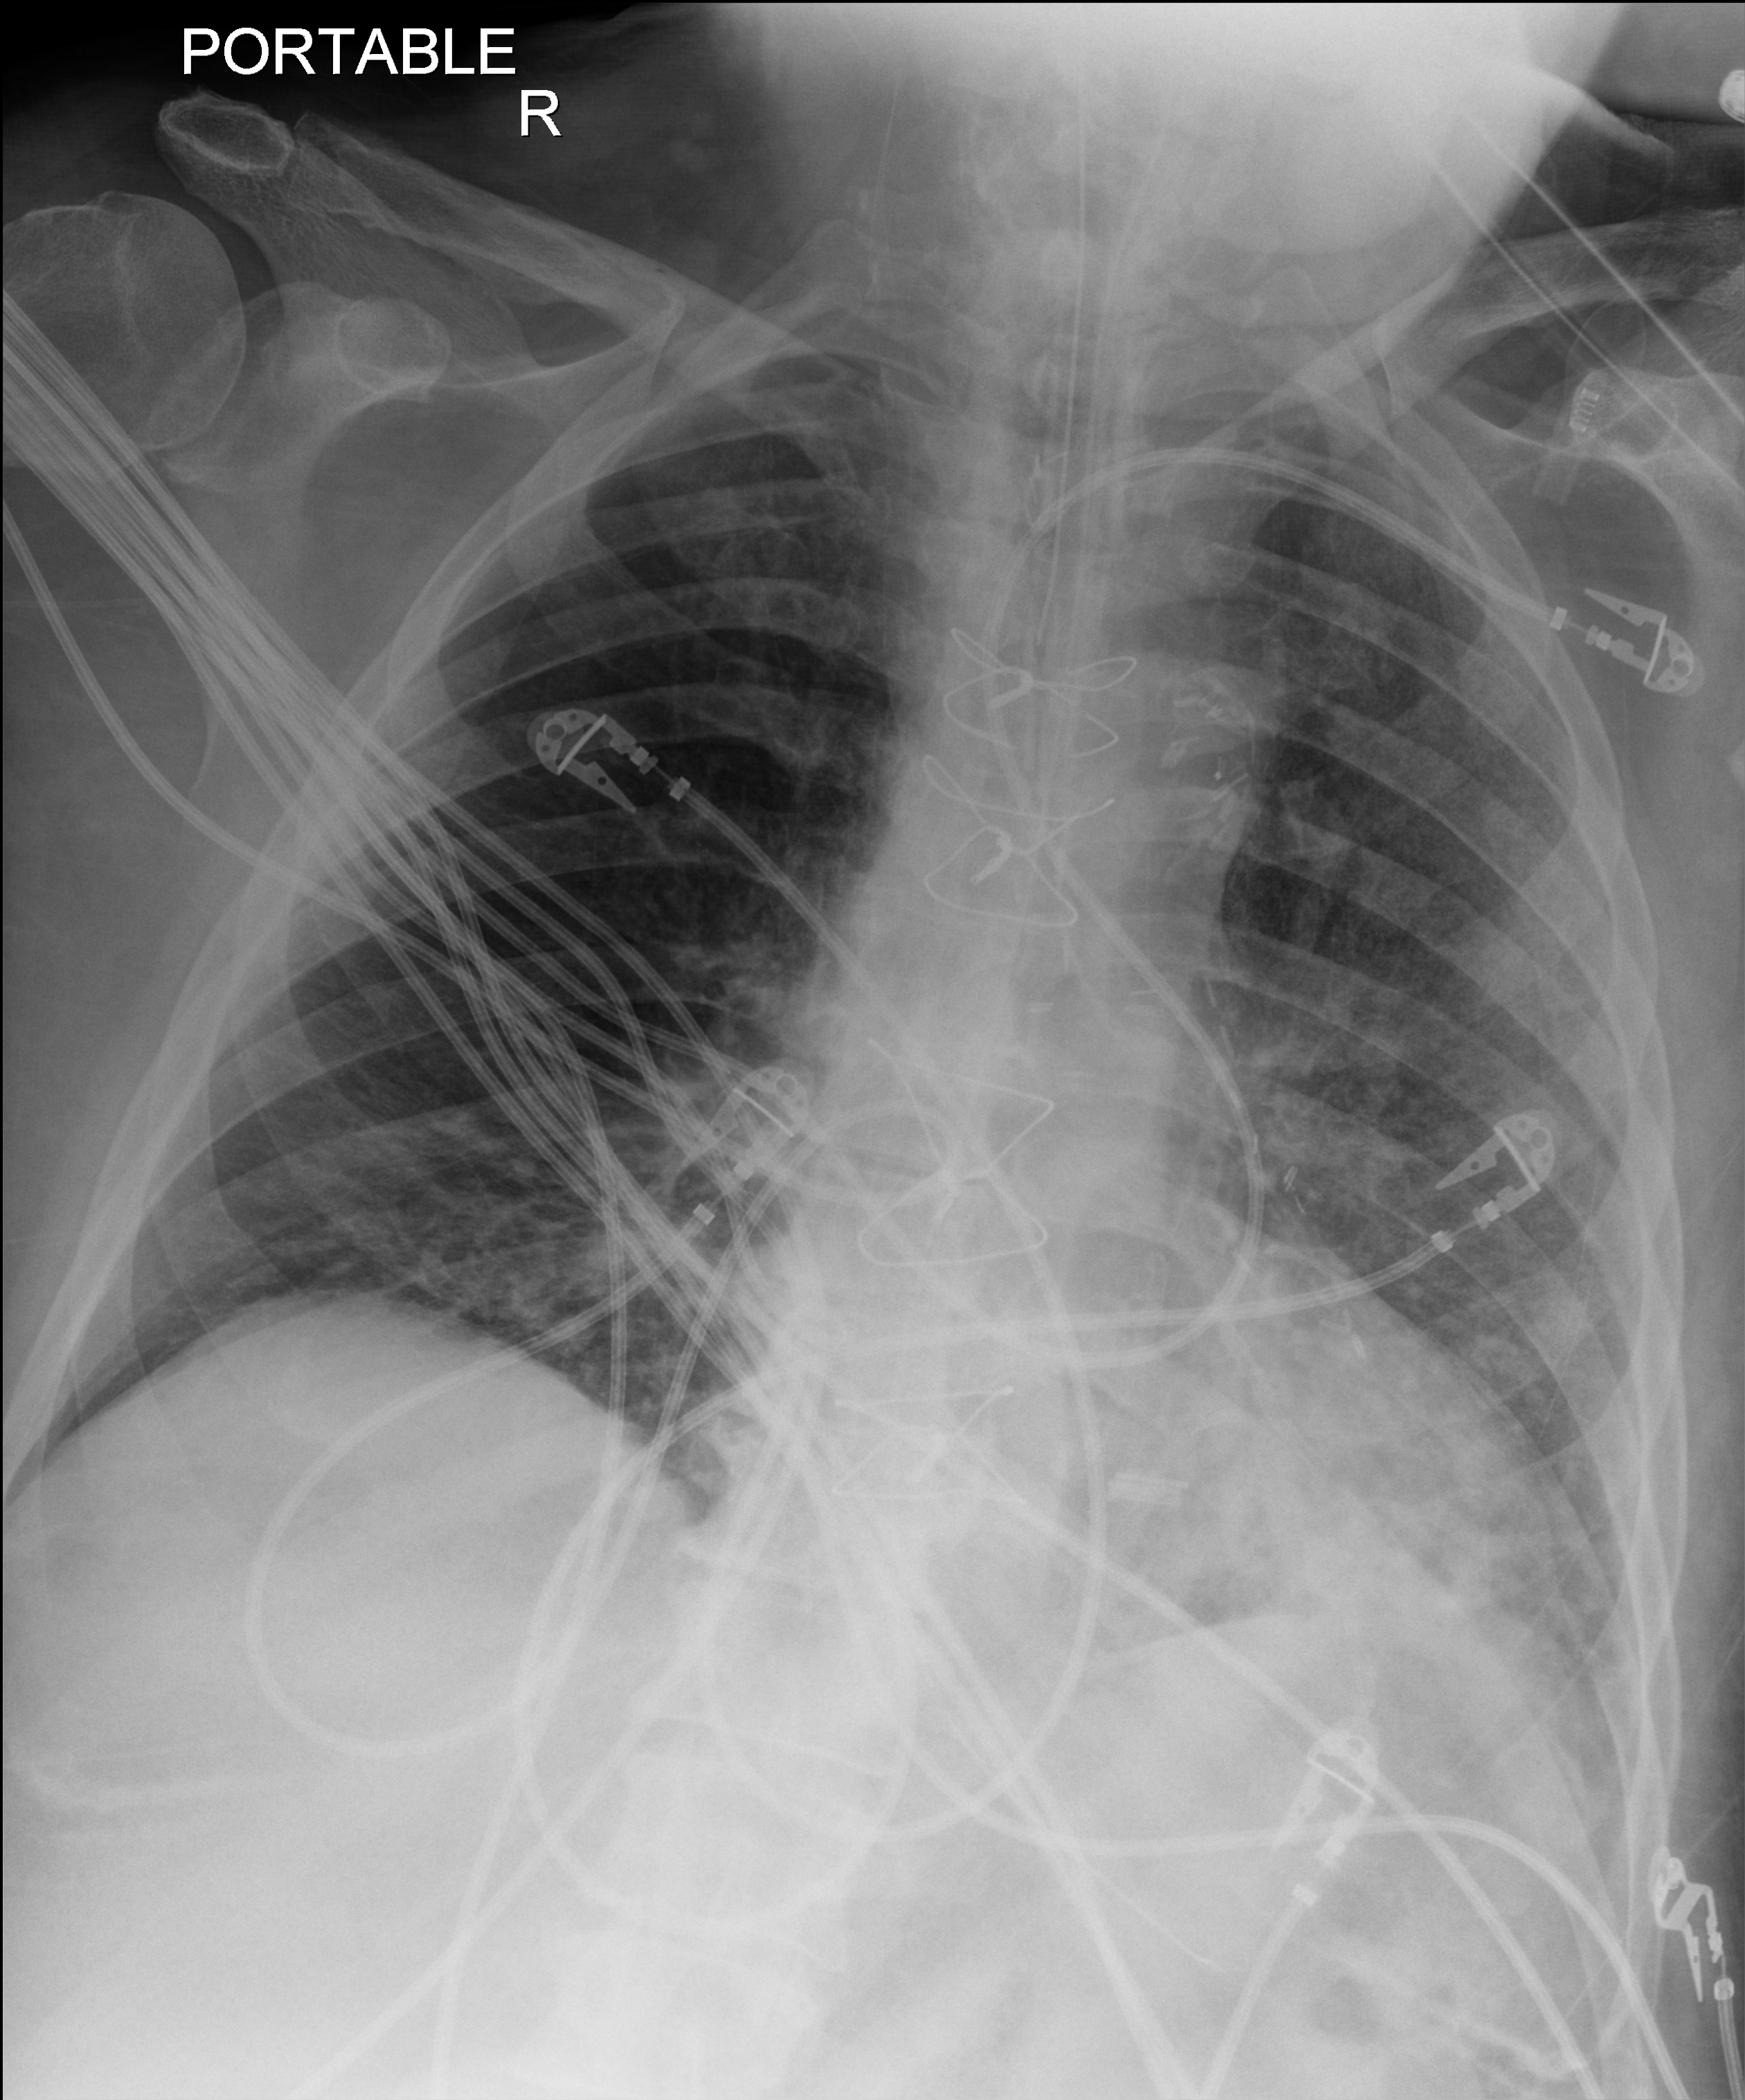
Portable chest radiograph, anteroposterior (AP) projection. Male patient hospitalised with COVID-19, age 60–74 years.
From the hospital-stay record, not from the radiograph (when in the stay this image was taken is not recorded):
- admitted to intensive care during this hospital stay: yes